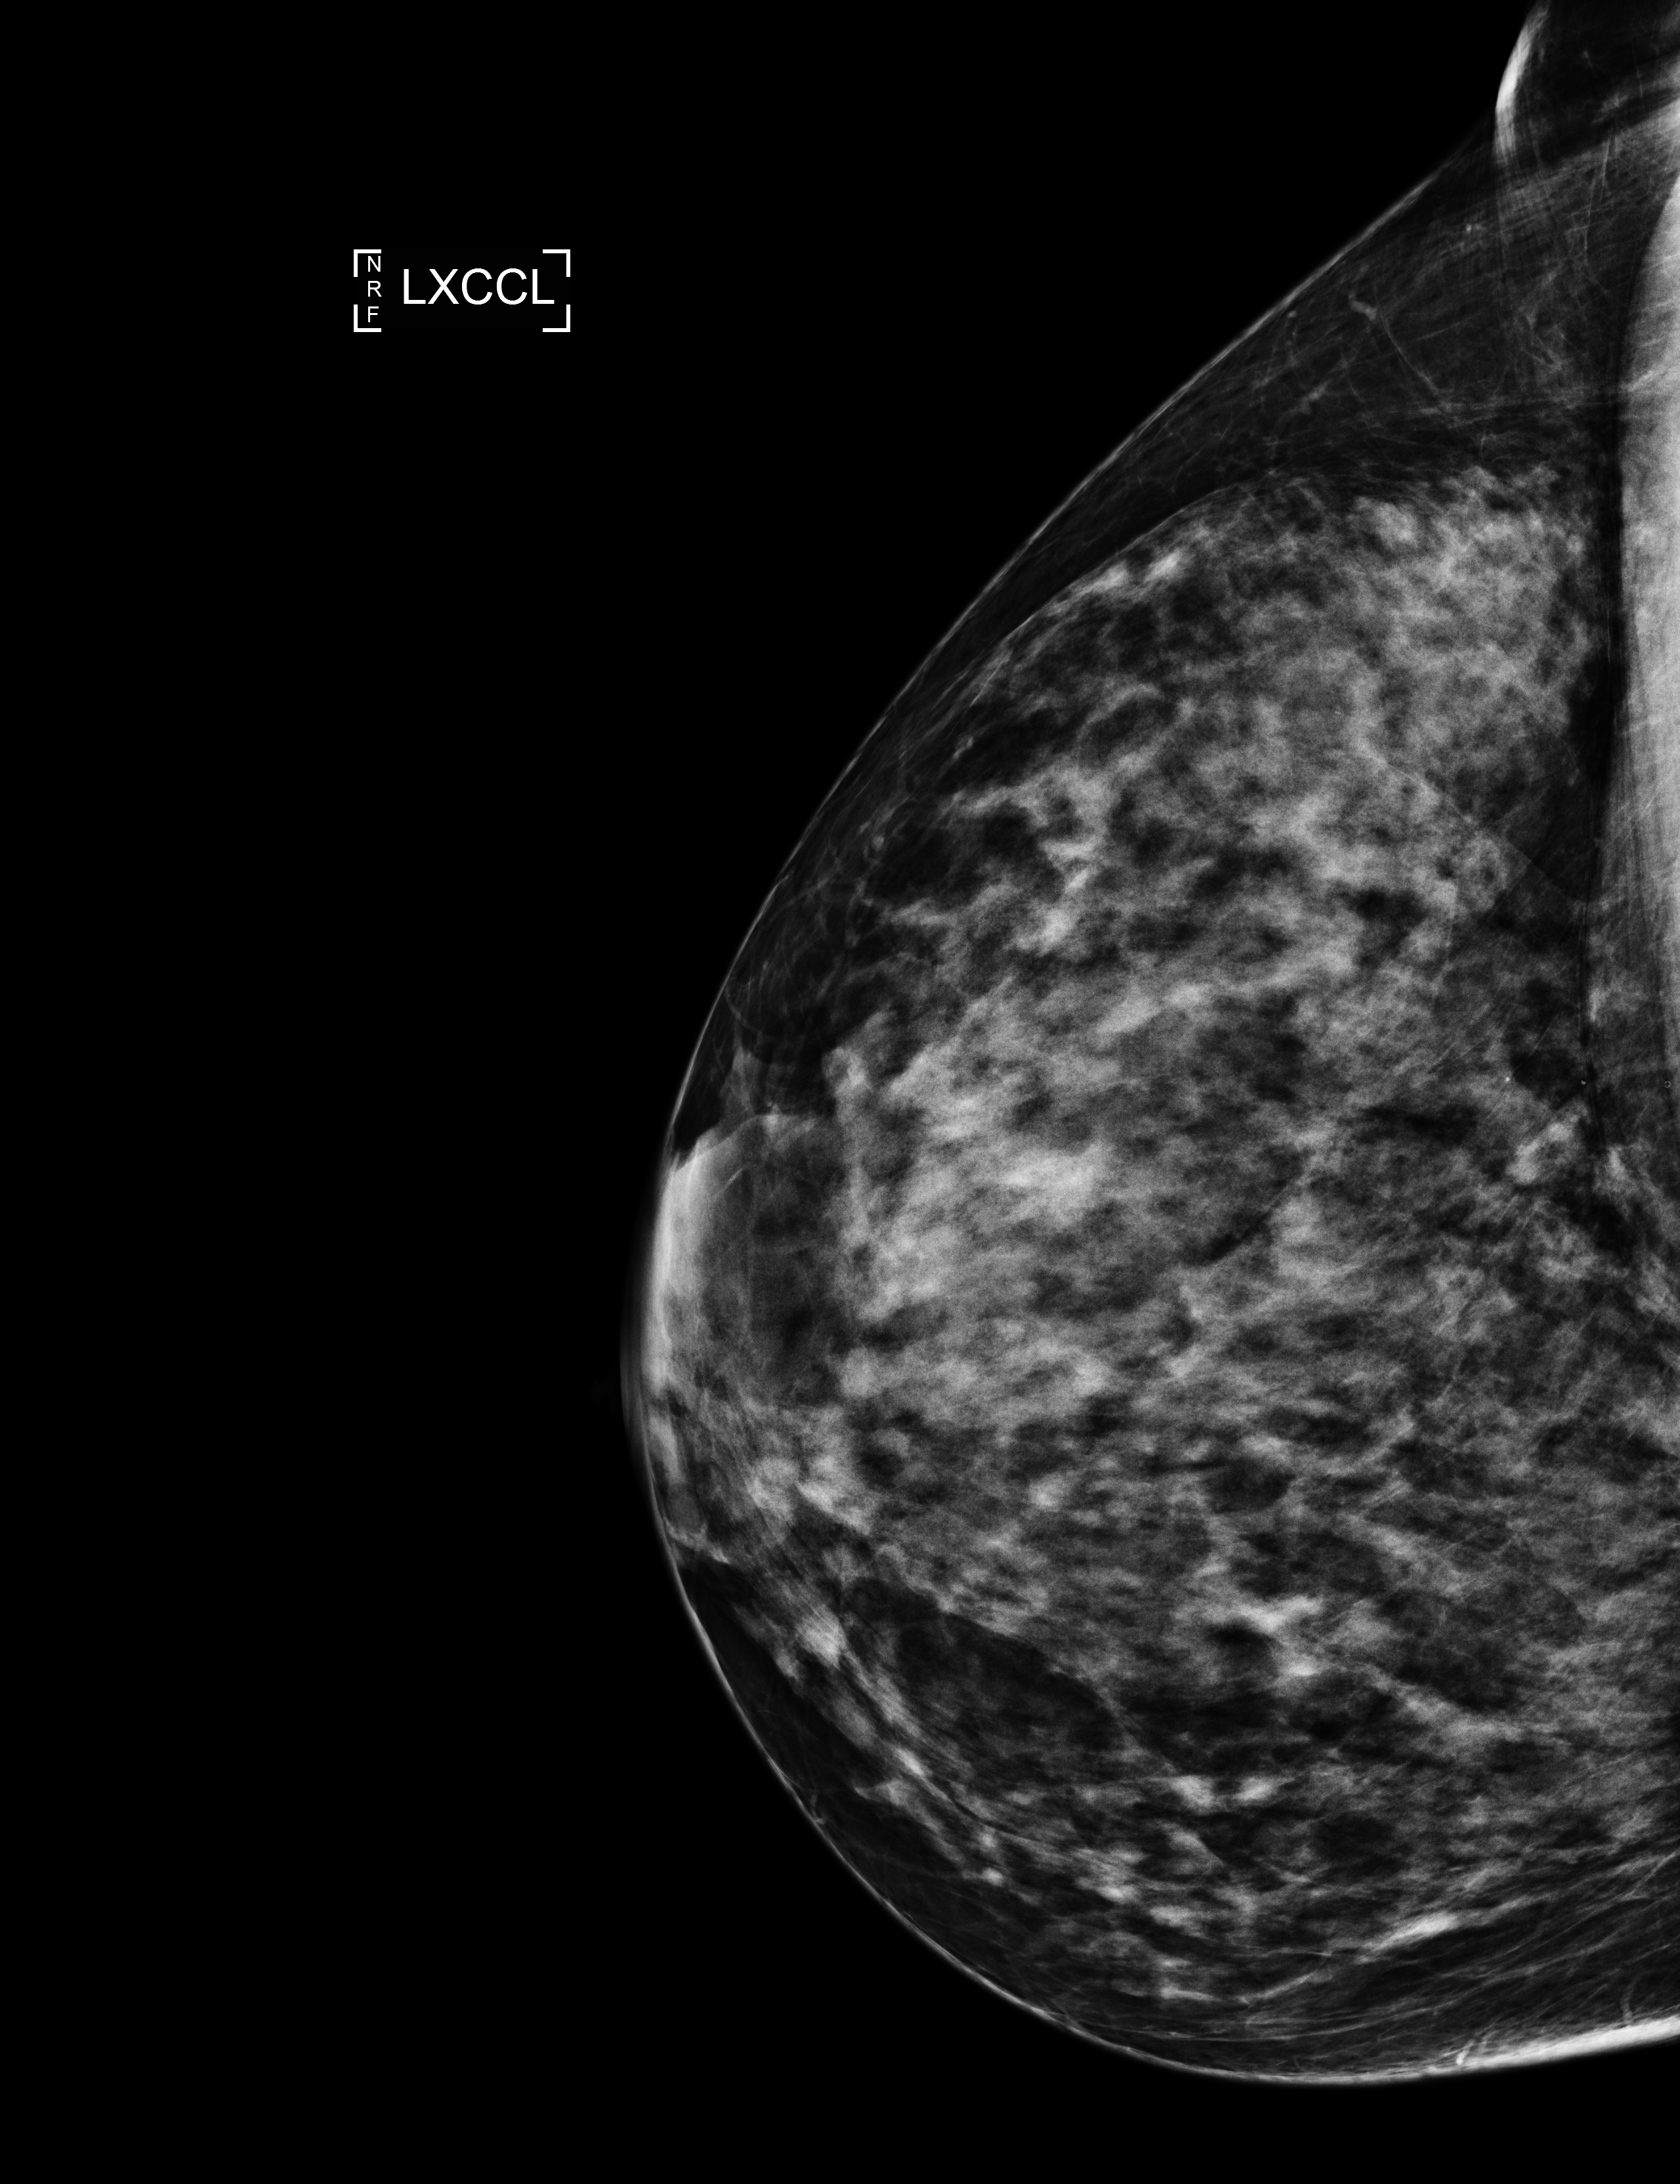
Full-field digital mammogram (FFDM); left breast; exaggerated CC view (lateral); annual screening mammography examination; system: Selenia Dimensions. Female patient, age 60 years.
- breast density at the screening exam (both breasts): extremely dense (BI-RADS density category d)
- final BI-RADS assessment for this screening round (tomosynthesis exam, both breasts): category 1
- recall: no recall after this screen